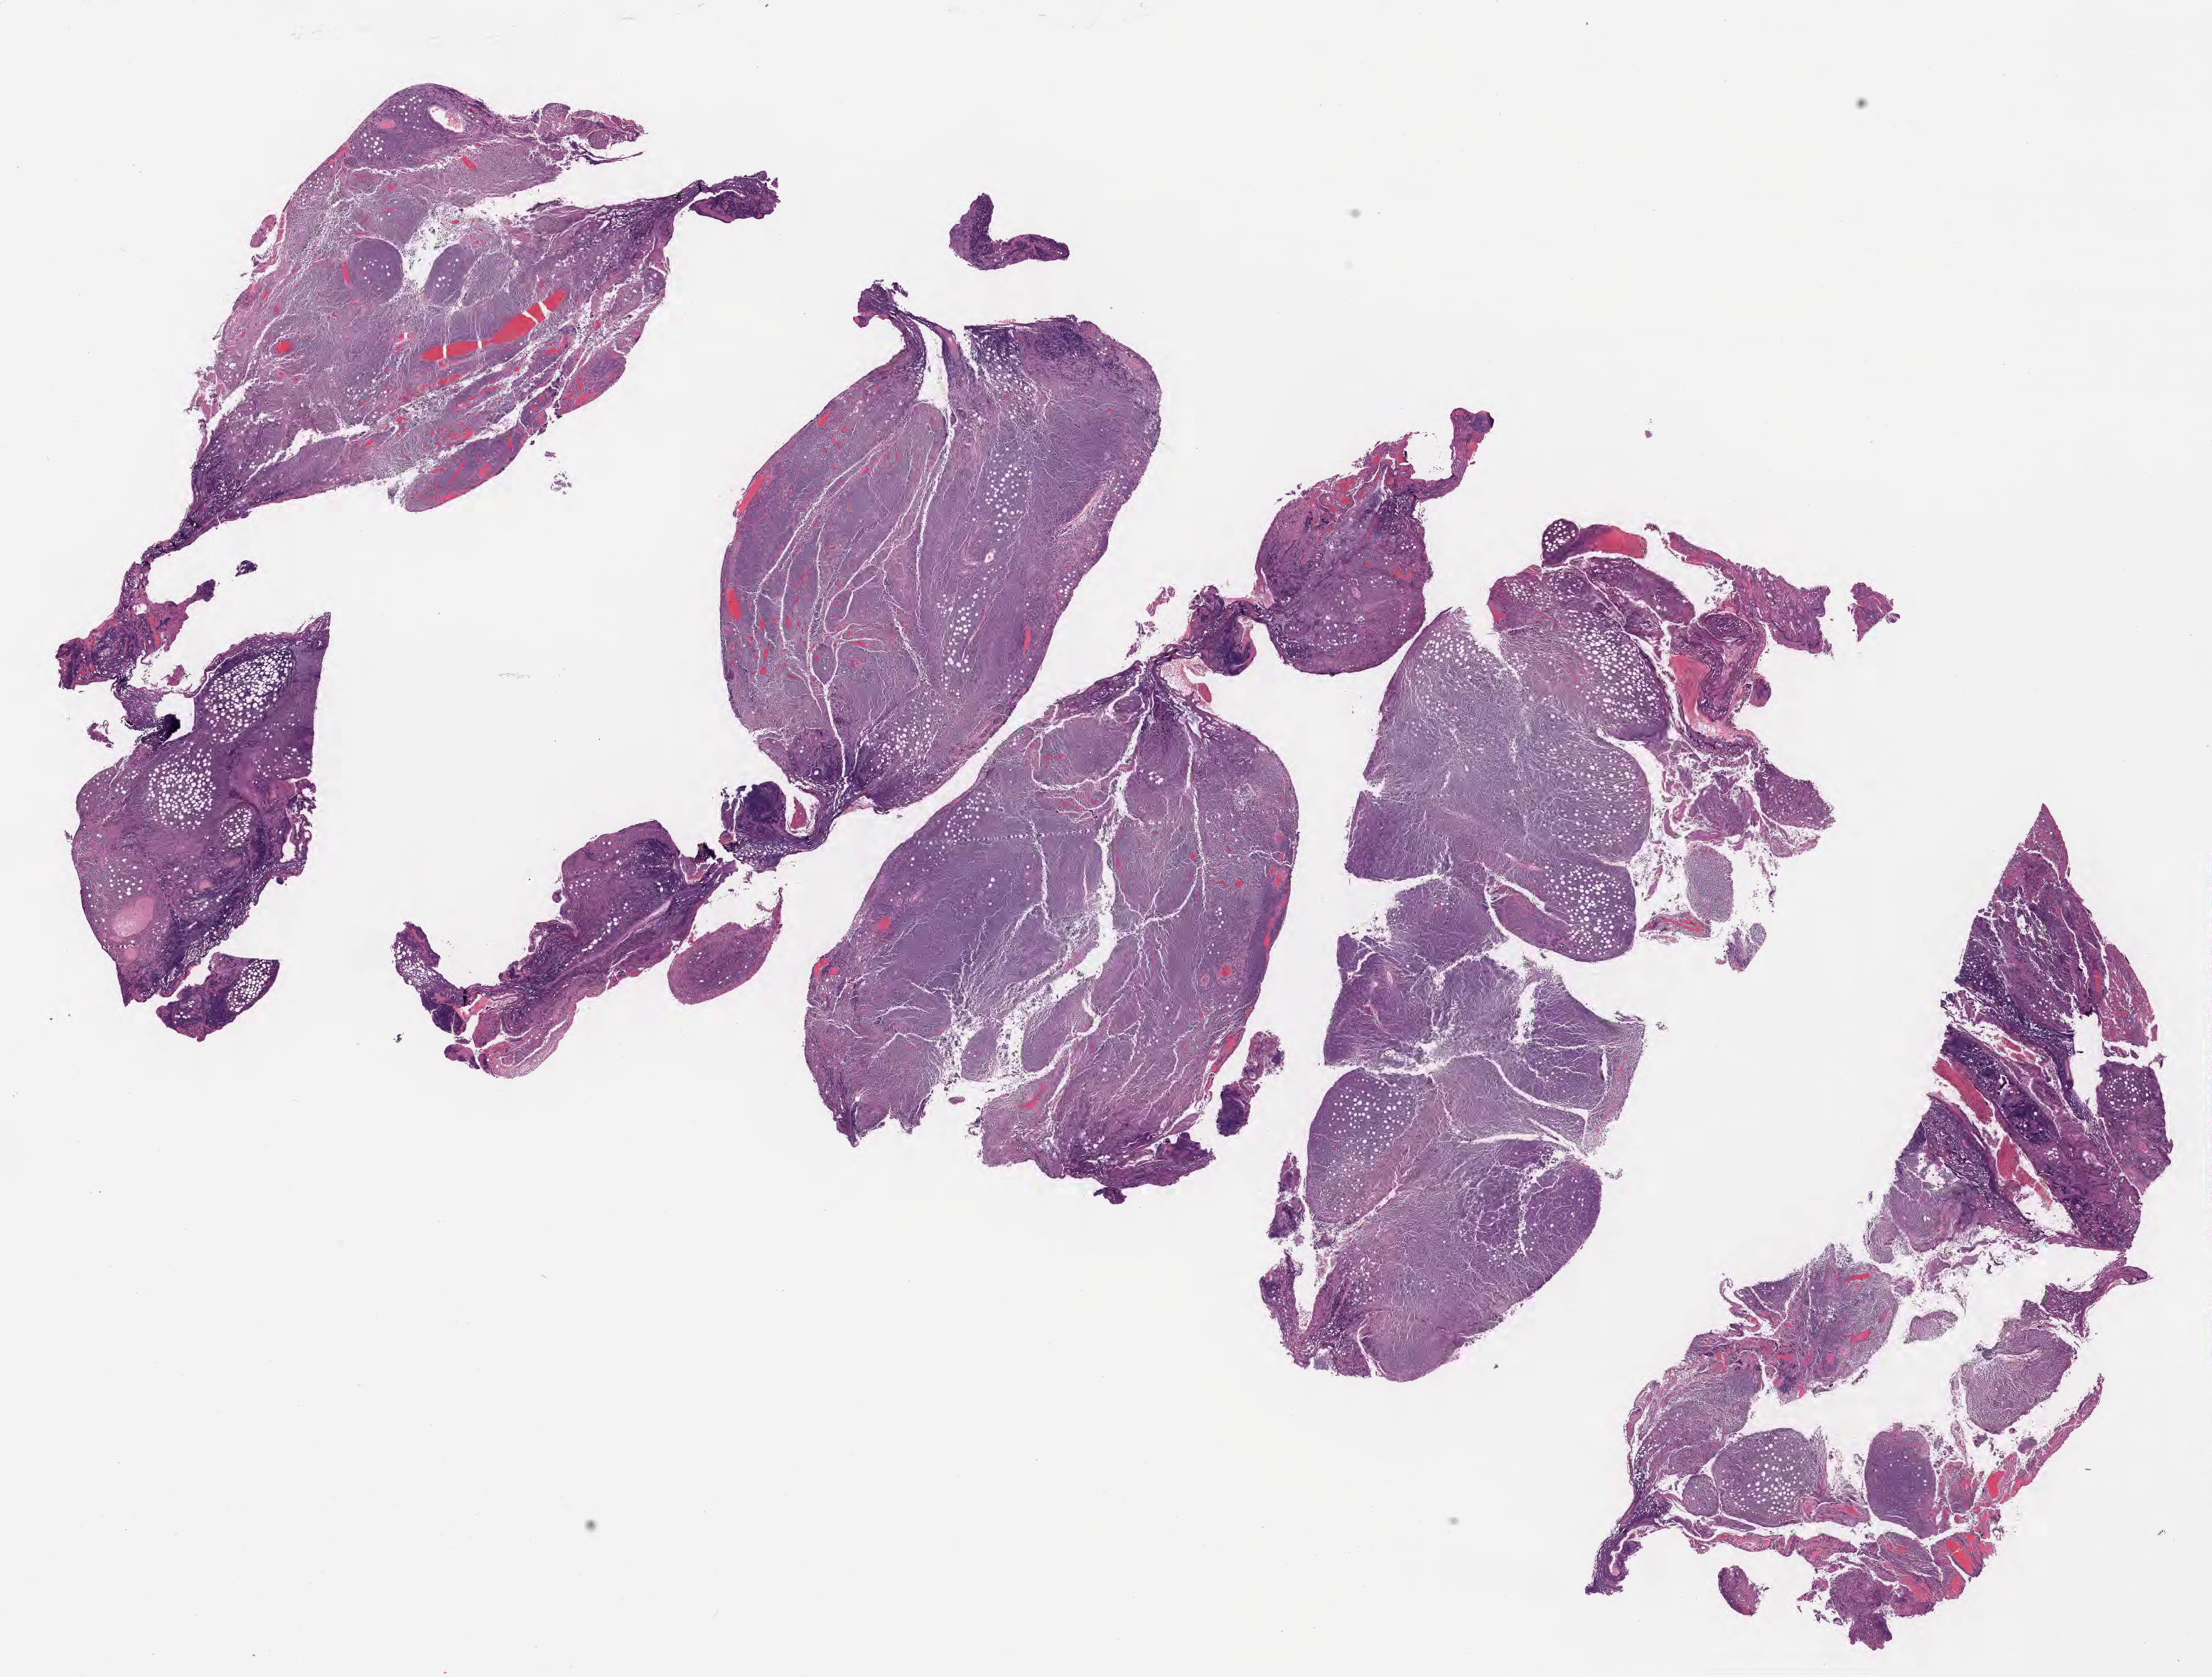
Whole-slide image, H&E stain — shown as a low-resolution overview of the whole scanned area (about 25.1 x 19.1 mm), specimen: tumor tissue, site: peritoneum. Male patient; age at initial diagnosis 8 years.
• histologic diagnosis: Burkitt lymphoma, NOS